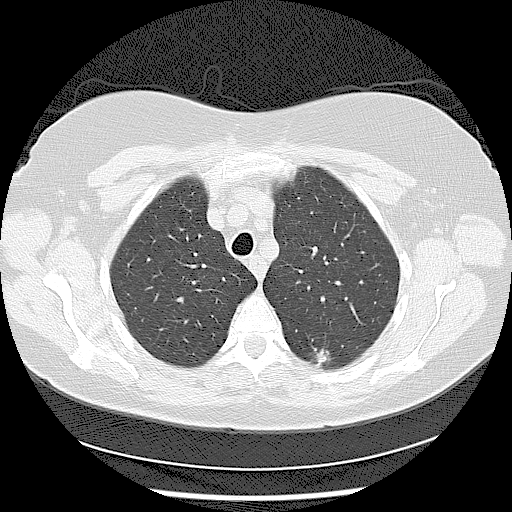
Low-dose screening chest CT, axial slice; baseline screening round; lung window (W 1500 / L -600 HU); 2.5 mm slice thickness; lung (sharp) reconstruction kernel (LUNG); 120 kVp; slice 24 of 116 in the series. Female, age 56 years at enrolment. Current smoker at enrolment.
• Lesion marked by an expert reader, bounding box [x1, y1, x2, y2] px = [296, 332, 346, 379].
• The screening reader recorded 2 non-calcified nodules or masses ≥4 mm on this exam; which of them this box marks is not recorded.
• Participant outcome: lung cancer diagnosed 638 days after this screen — adenocarcinoma, NOS, left lower lobe, moderately differentiated (G2), stage IIA (AJCC 6th edition), 15 mm at pathology.